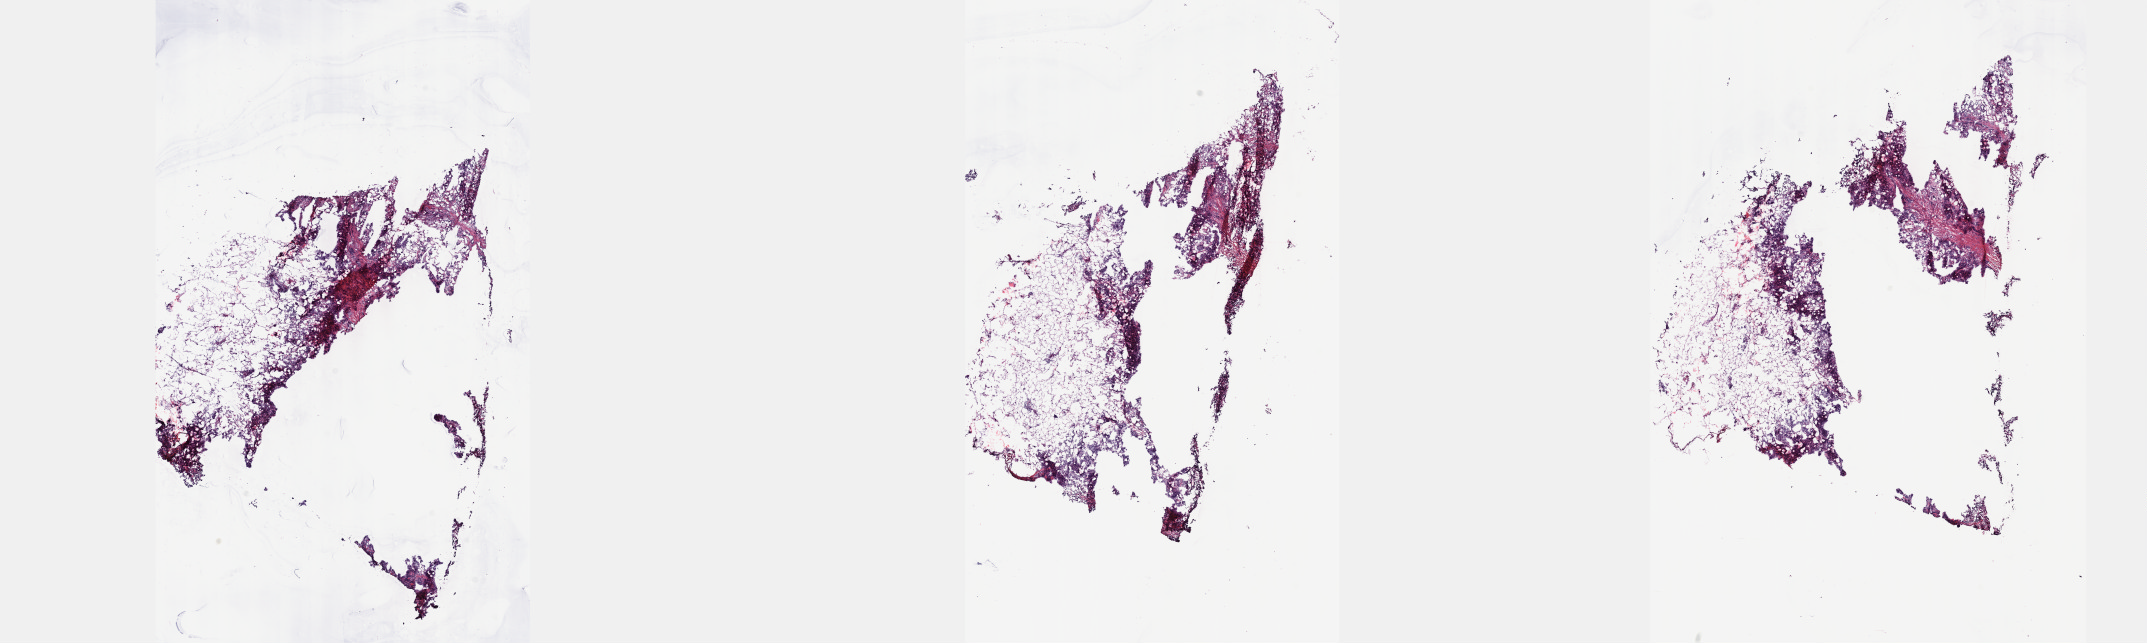
H&E-stained whole-slide image, shown as a low-resolution overview of the whole scanned area (about 34.7 x 10.4 mm), frozen section from the top of the tissue portion, breast, primary tumour sample. Patient: female, age at initial diagnosis 62 years. Slide review estimates, as recorded: tumour cells 100%, tumour nuclei 65%, normal cells 0%, stromal cells 0%, necrosis 0%. Inflammatory infiltration, as recorded: lymphocyte infiltration 4%, monocyte infiltration 0%, neutrophil infiltration 0%.
Diagnosis: Infiltrating duct carcinoma, NOS. AJCC pathologic stage: IIB (7th edition). Laterality: right.